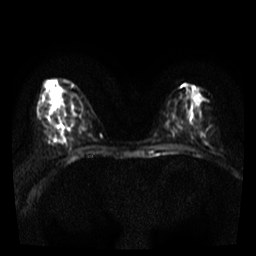
Breast MRI, one axial slice; slice 13 of 36 in the series (ordered by position); diffusion-weighted series; image 2 of 4 stored at this slice position (different b-values; order by instance number); 3 T; 5 mm slice thickness; 256 × 256 image matrix. Female patient.
Annotated regions visible in this slice (manually delineated by an expert):
- tumour on diffusion-weighted imaging: bounding box (x1, y1, x2, y2) in pixels: (51, 110, 54, 114)